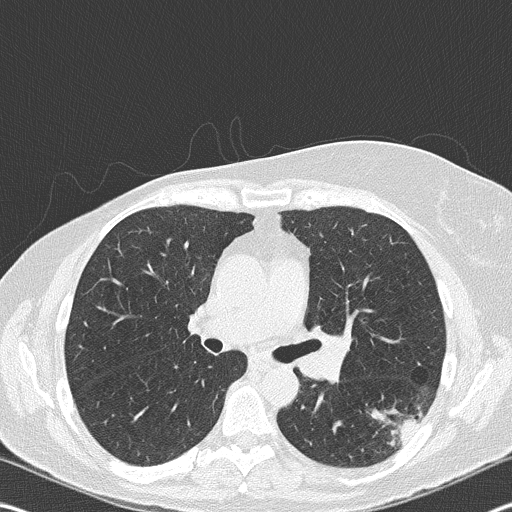
Low-dose screening chest CT, one axial slice; slice 107 of 177 in the series (ordered by position); lung window (W 1500 / L -600 HU); 2 mm slice thickness; 512 × 512 image matrix, field of view 342 × 342 mm.
Annotated regions visible in this slice (manually delineated by an expert):
- lesion 1 (tumor): bounding box (x1, y1, x2, y2) in pixels: (371, 410, 422, 446)
- lesion 2 (nodule, hilum of left lung): (301, 340, 344, 378)